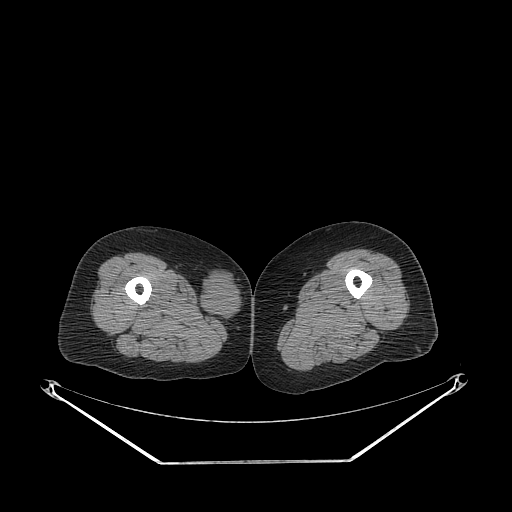
CT of an extremity soft-tissue mass (from a PET/CT study), one axial slice; slice 231 of 311 in the series (ordered by position); reconstruction kernel STANDARD; 140 kVp; soft-tissue window (W 400 / L 40 HU); 3.75 mm slice thickness; 512 × 512 image matrix, field of view 500 × 500 mm. Female patient. From the clinical record (not read from this slice): histological type: leiomyosarcoma; grade: intermediate; site of the primary tumour: parascapusular.
Outlined on this slice (expert contour drawn on MRI and transferred to this co-registered scan by the dataset authors):
- gross tumour volume including surrounding oedema: box from (x=201, y=269) to (x=241, y=323) px
- gross tumour volume (mass): (x=201, y=269)–(x=241, y=321)